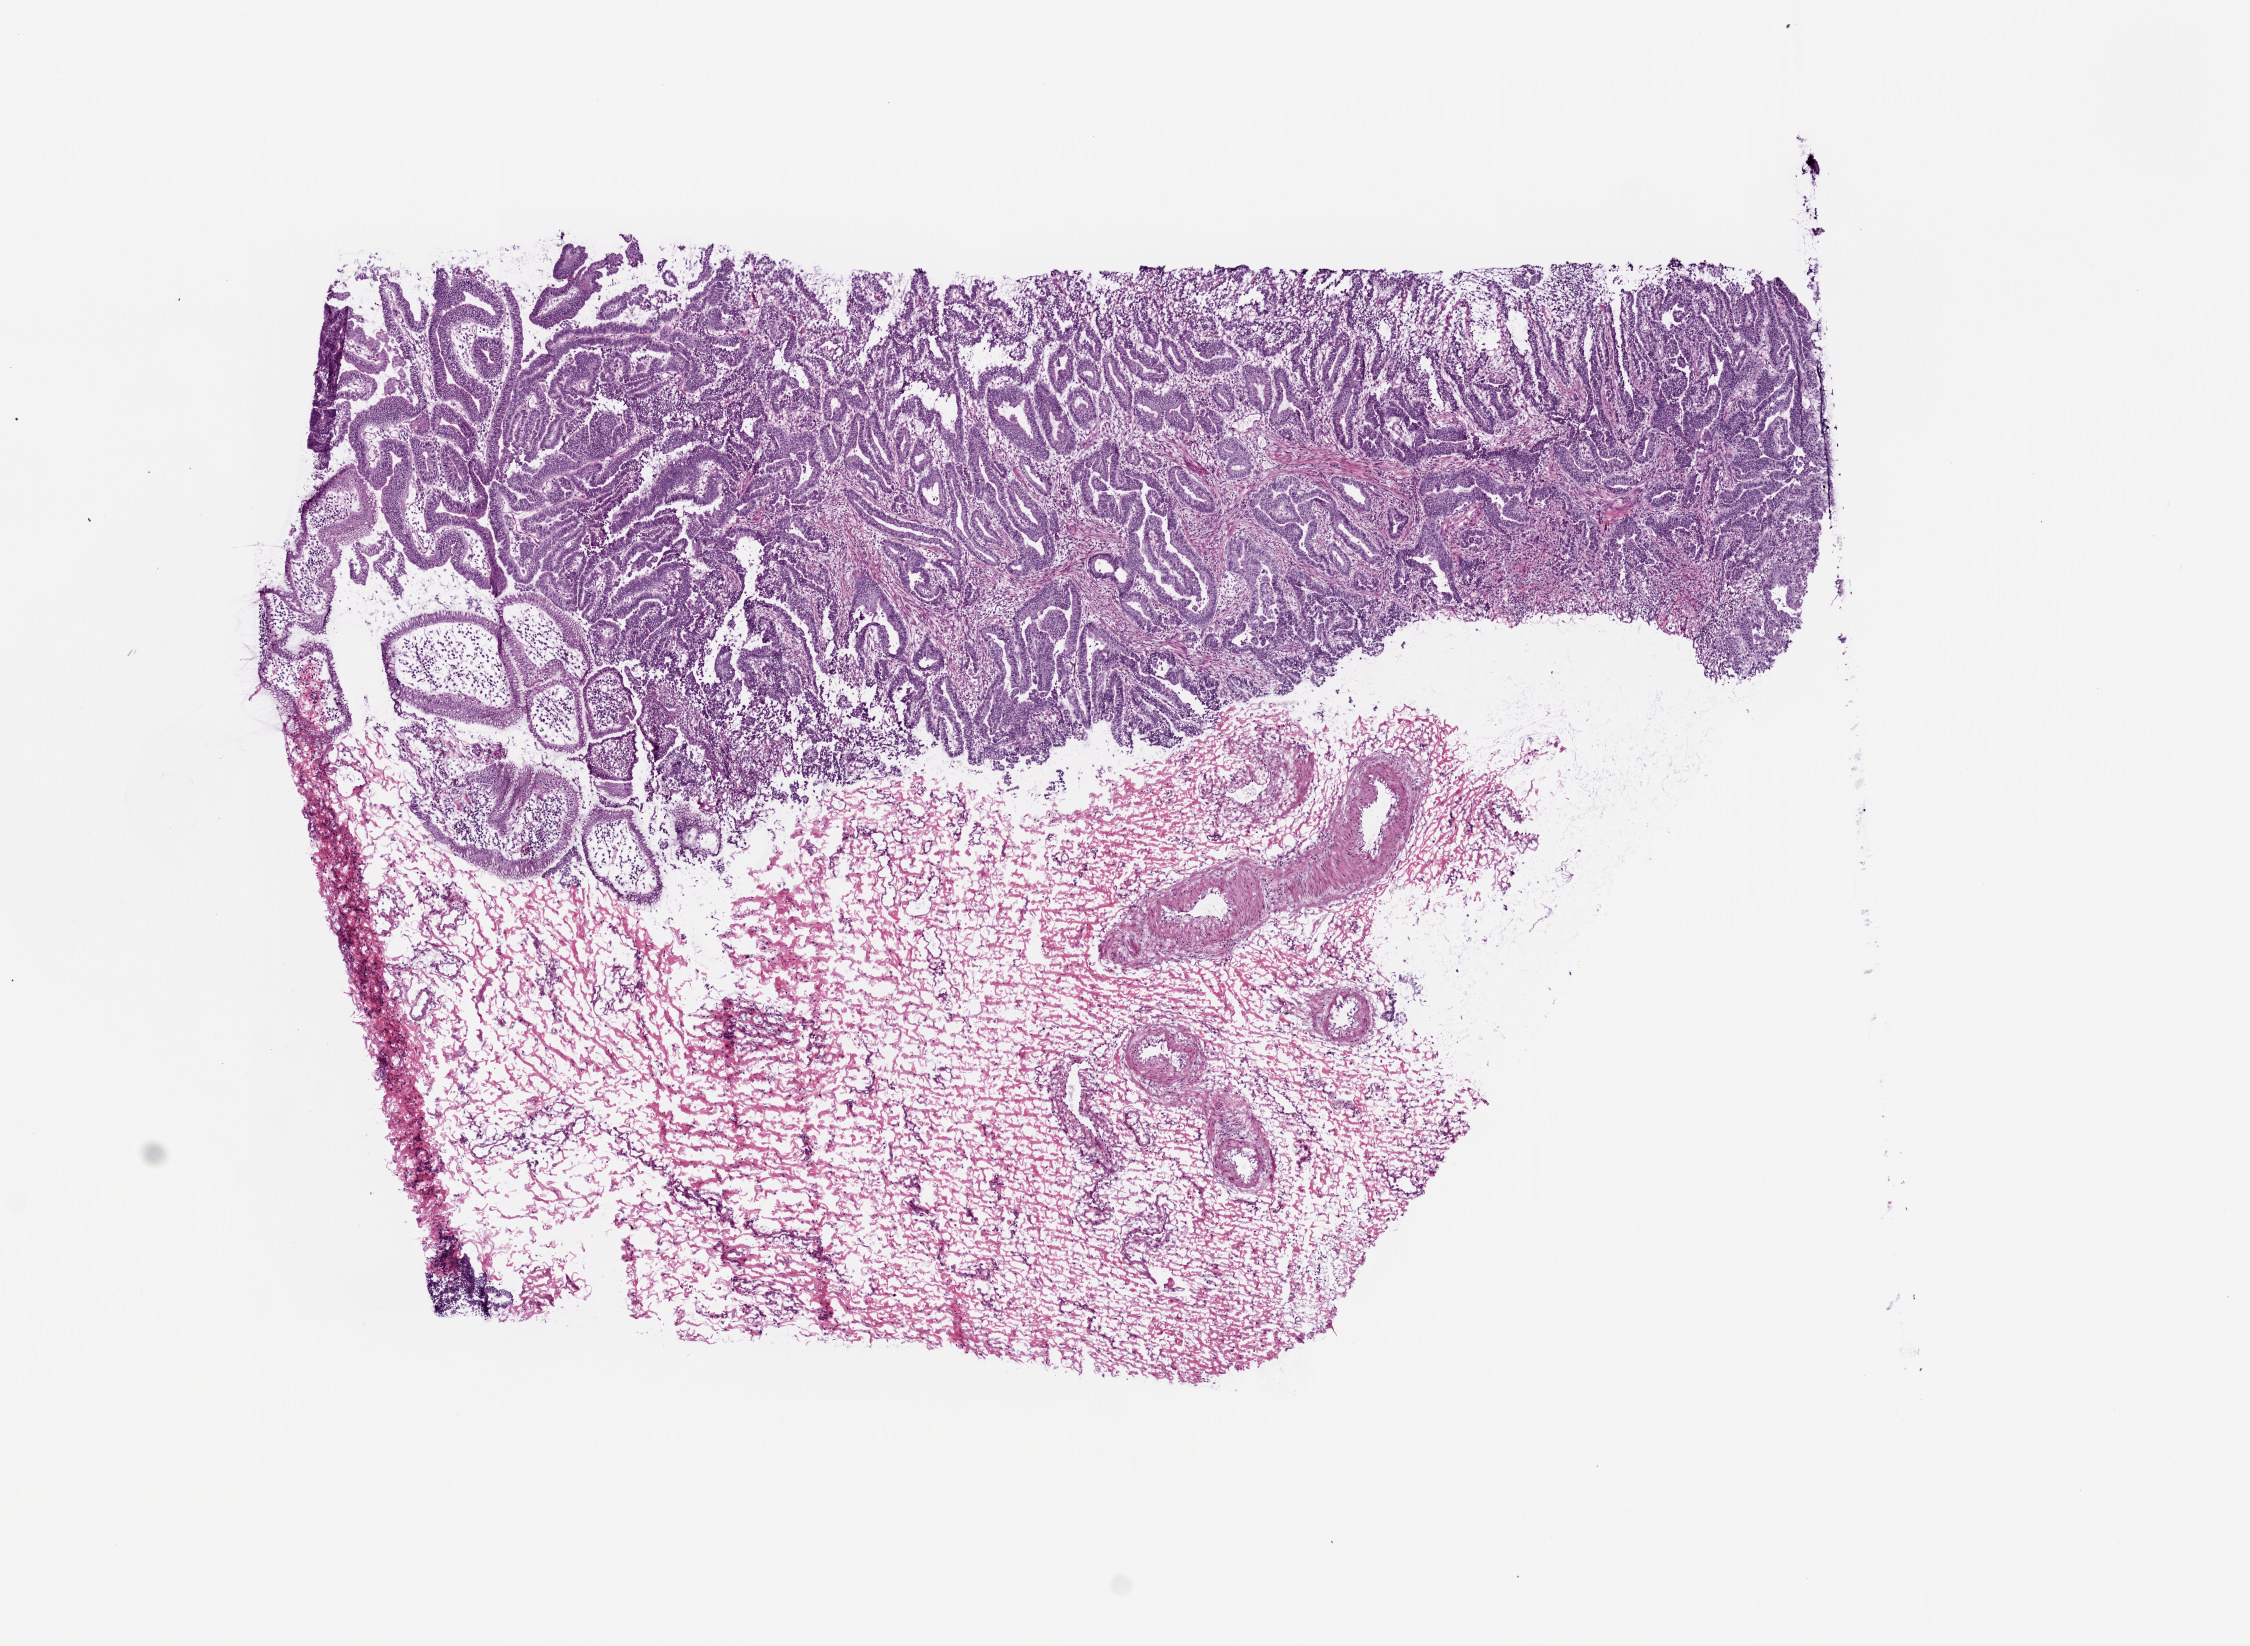
Digitized H&E-stained tissue section (whole slide), shown as a low-resolution overview of the whole scanned area (about 9.0 x 6.6 mm). Frozen section from the bottom of the tissue portion. Primary tumour sample from the stomach. Patient: male, age at initial diagnosis 73 years. Histologic grade: G2 (moderately differentiated). Pathologist review of this section (percent, as recorded): tumour cells 32%, tumour nuclei 75%, normal cells 10%, stromal cells 50%, necrosis 8%.
- AJCC pathologic stage: IA (5th edition)
- pathologic diagnosis: Adenocarcinoma, intestinal type (gastric antrum)
- TNM: T1 N0 M0